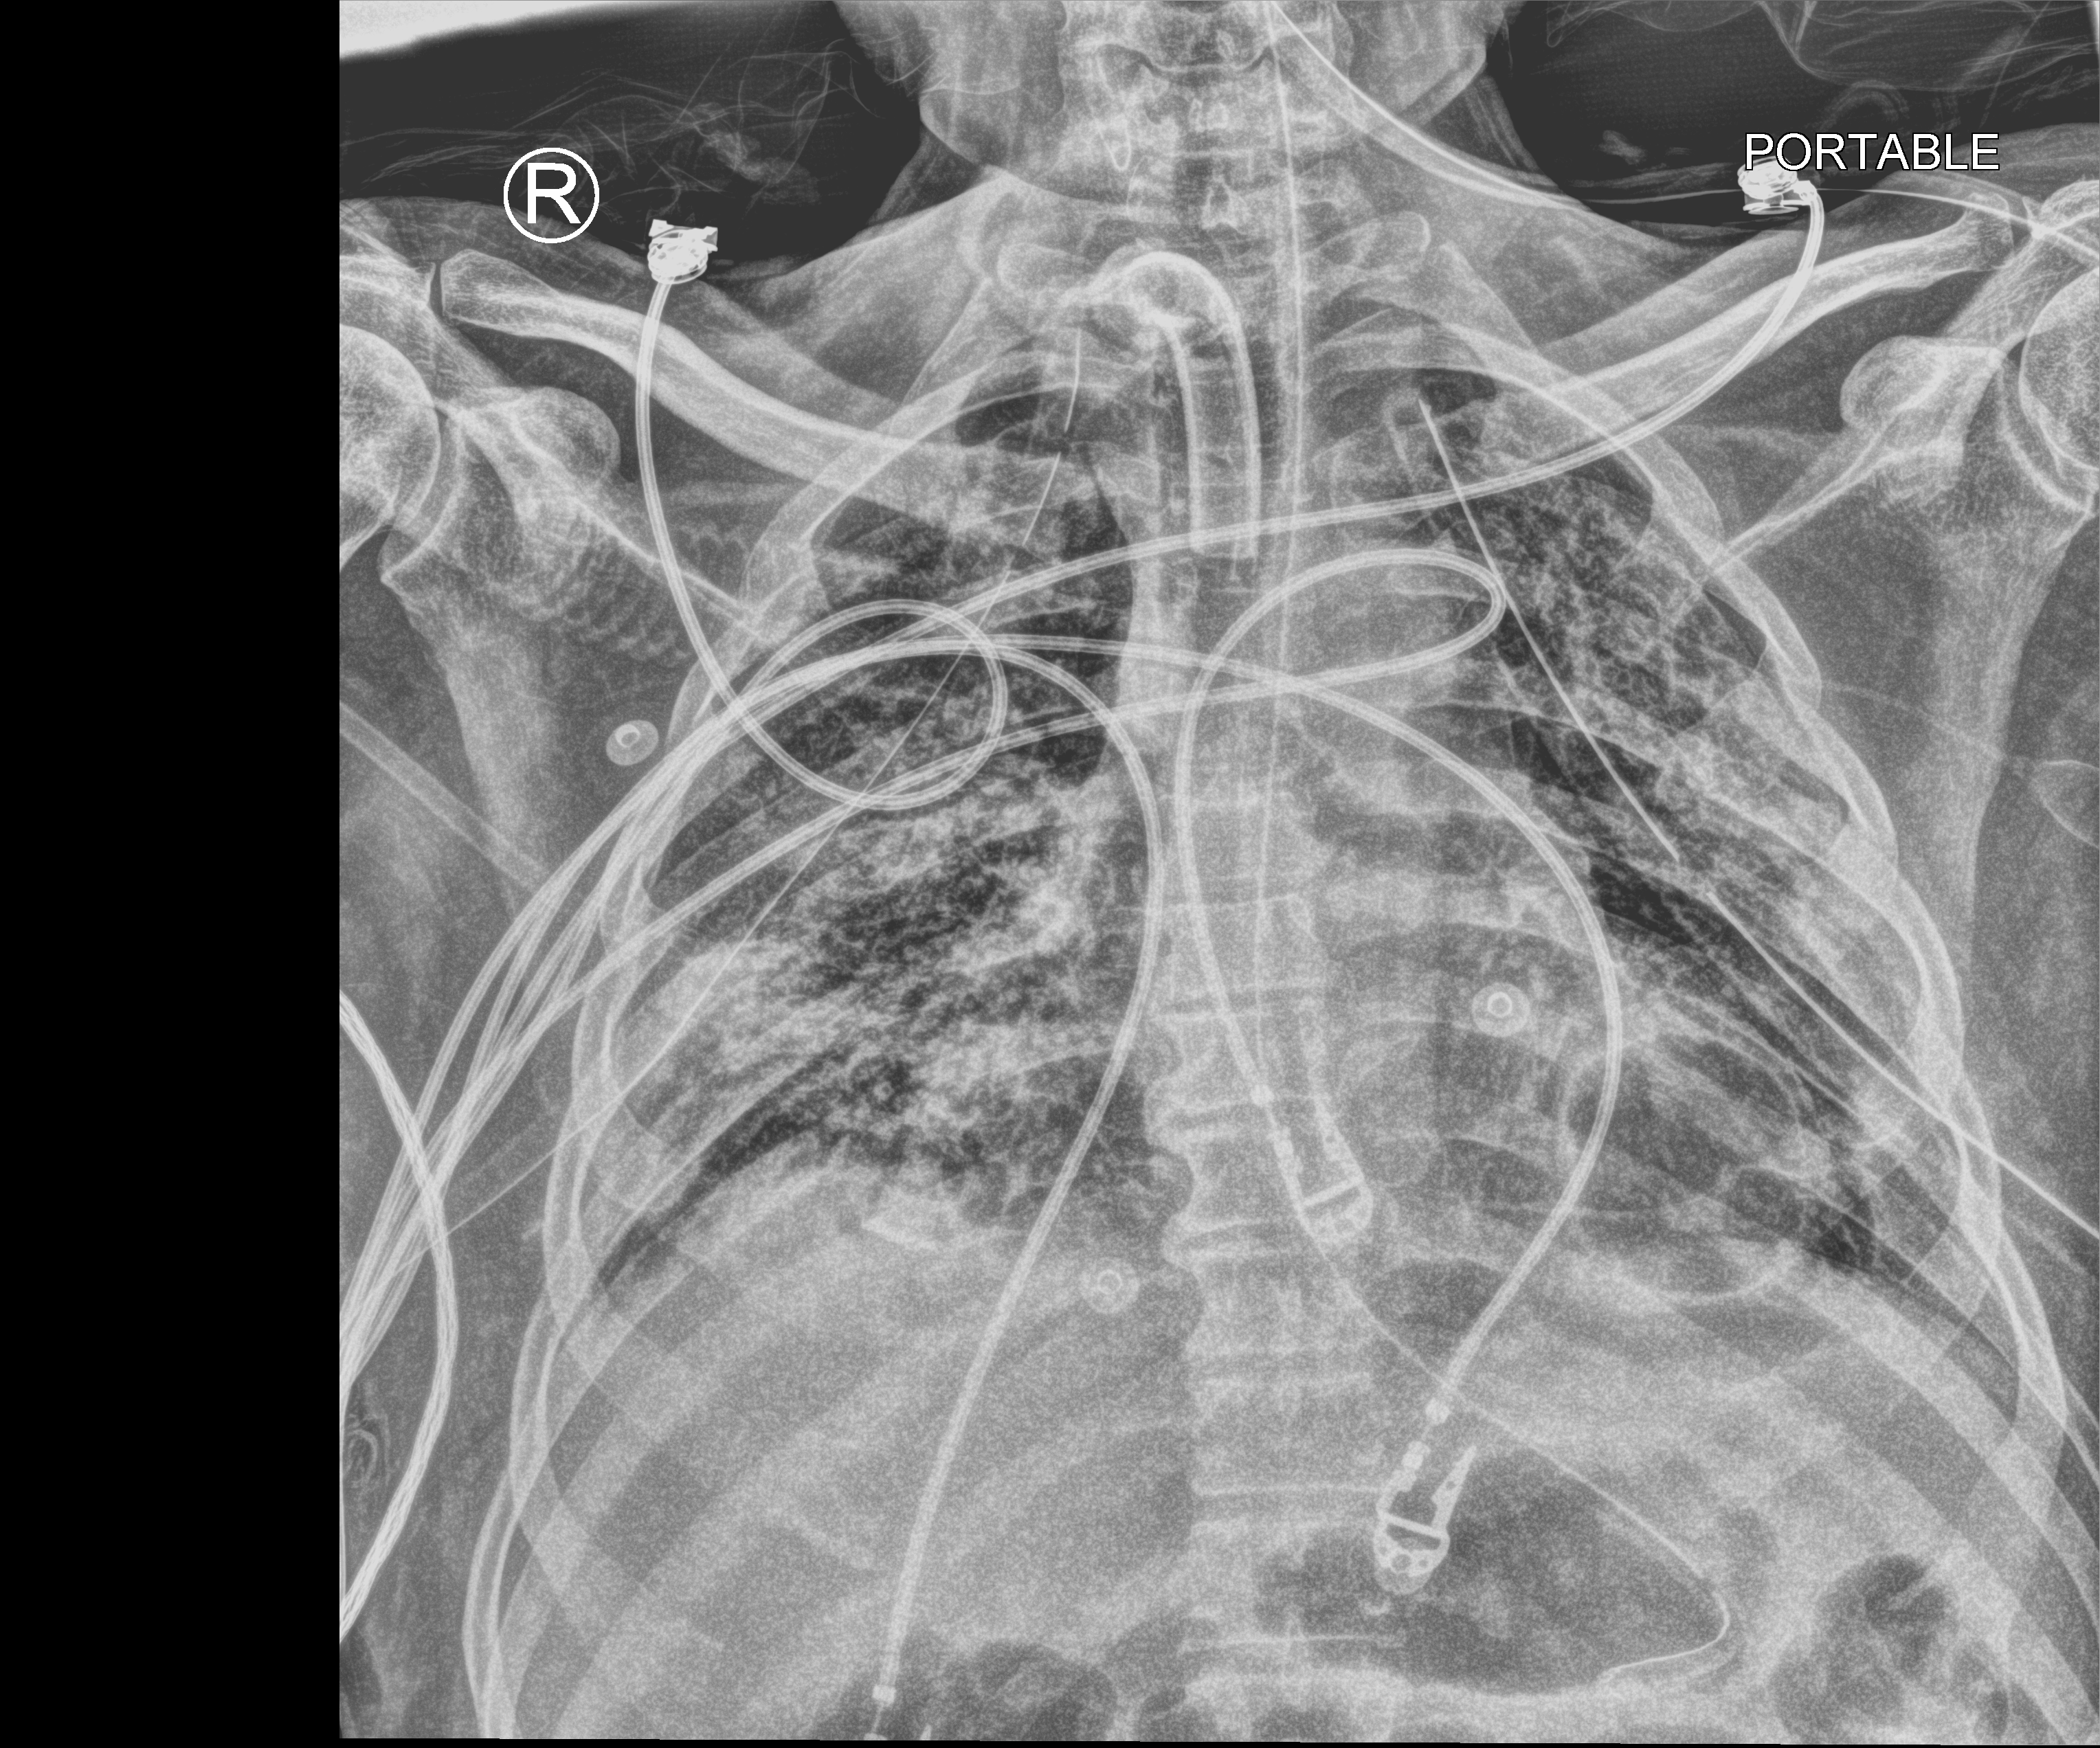
Bedside chest radiograph (computed radiography); anteroposterior (AP) projection. Male patient hospitalised with COVID-19, age 18–59 years.
From the hospital-stay record, not from the radiograph (when in the stay this image was taken is not recorded): mechanically ventilated during this hospital stay: yes; diabetes (admission record): no.